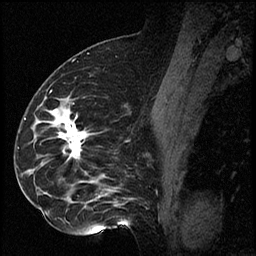
Breast MRI (dynamic contrast-enhanced), one sagittal slice; slice 39 of 60 in the series (ordered by position); dynamic contrast-enhanced series, image 2 of 2 at this slice position (ordered by acquisition); 1.5 T; TE 4.2 ms, TR 17.3 ms; 2 mm slice thickness; 256 × 256 image matrix. Female patient. From the clinical record (not read from this slice): setting: breast cancer imaged before/during neoadjuvant chemotherapy; receptor status: HR-positive, HER2-negative.
Structures marked on this image (semi-automatic segmentation, software-assisted and operator-edited):
- analysis volume of interest (the breast-tissue region the enhancement analysis was run in; not a lesion): bounding box [x1, y1, x2, y2] px = [41, 94, 115, 223]
- tumour enhancement mask (voxels above the 100 % enhancement threshold inside the analysis volume of interest): [58, 114, 84, 158]